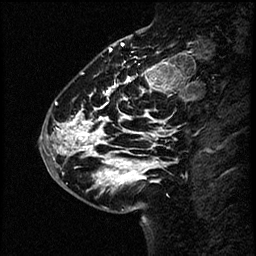
Breast MRI (dynamic contrast-enhanced), one sagittal slice; position 21 of 60 along the scan axis; dynamic contrast-enhanced study with each time point stored as its own series, time point 2 of 4 at this slice position (early post-contrast, ordered by acquisition time); 1.5 T; TE 4.2 ms, TR 17.6 ms; 2 mm slice thickness; 256 × 256 image matrix, field of view 200 × 200 mm. Patient: female, 43 years. From the clinical record (not read from this slice): setting: breast cancer imaged before/during neoadjuvant chemotherapy.
Annotated regions visible in this slice (semi-automatic segmentation, software-assisted and operator-edited):
- analysis volume of interest (the breast-tissue region the enhancement analysis was run in; not a lesion): bounding box <44,56,169,191> (left, top, right, bottom; pixels)
- tumour enhancement mask (voxels above the 100 % enhancement threshold inside the analysis volume of interest): <47,71,169,190>